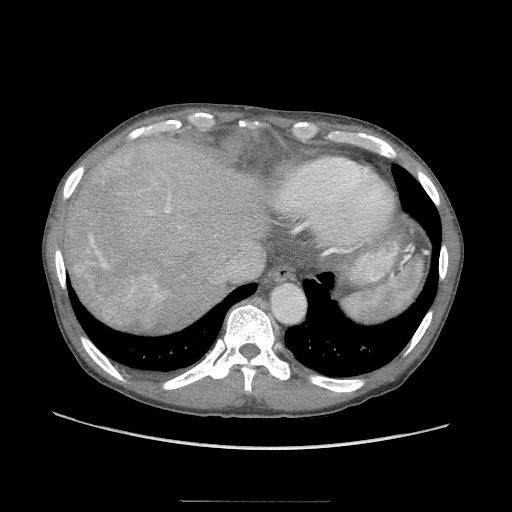
Contrast-enhanced abdominal CT (liver protocol), one axial slice. Reconstruction kernel STANDARD. 120 kVp. Soft-tissue window (W 400 / L 40 HU). 512 × 512 image matrix. From the clinical record (not read from this slice): diagnosis: hepatocellular carcinoma (patient treated with transarterial chemoembolisation; whether this scan precedes or follows treatment is not stated here); TNM stage (as recorded): Stage-IIIA; Child-Pugh class: A; tumour differentiation: moderately differentiated; tumour size: 16 cm.
Outlined on this slice (semi-automatic segmentation, software-assisted and operator-edited):
- abdominal aorta: bounding box [x1, y1, x2, y2] px = [272, 285, 305, 321]
- liver parenchyma outside the tumour (the mass and vessels are separate outlines, so this box may not span the whole liver): [64, 128, 272, 332]
- liver vessels: [152, 284, 155, 287]